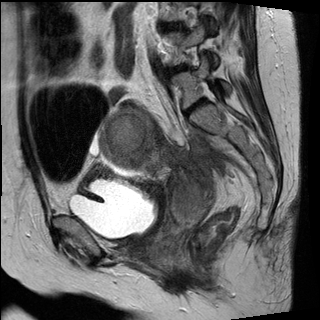
Pelvic MRI for cervical cancer, one sagittal slice; position 12 of 30 along the scan axis; T2-weighted; 1.5 T; TE 89 ms, TR 2930 ms; 4 mm slice thickness; 320 × 320 image matrix. Patient: female, 62 years.
Outlined on this slice (expert manual segmentation):
- uterus and cervix: box from (x=101, y=109) to (x=214, y=227) px